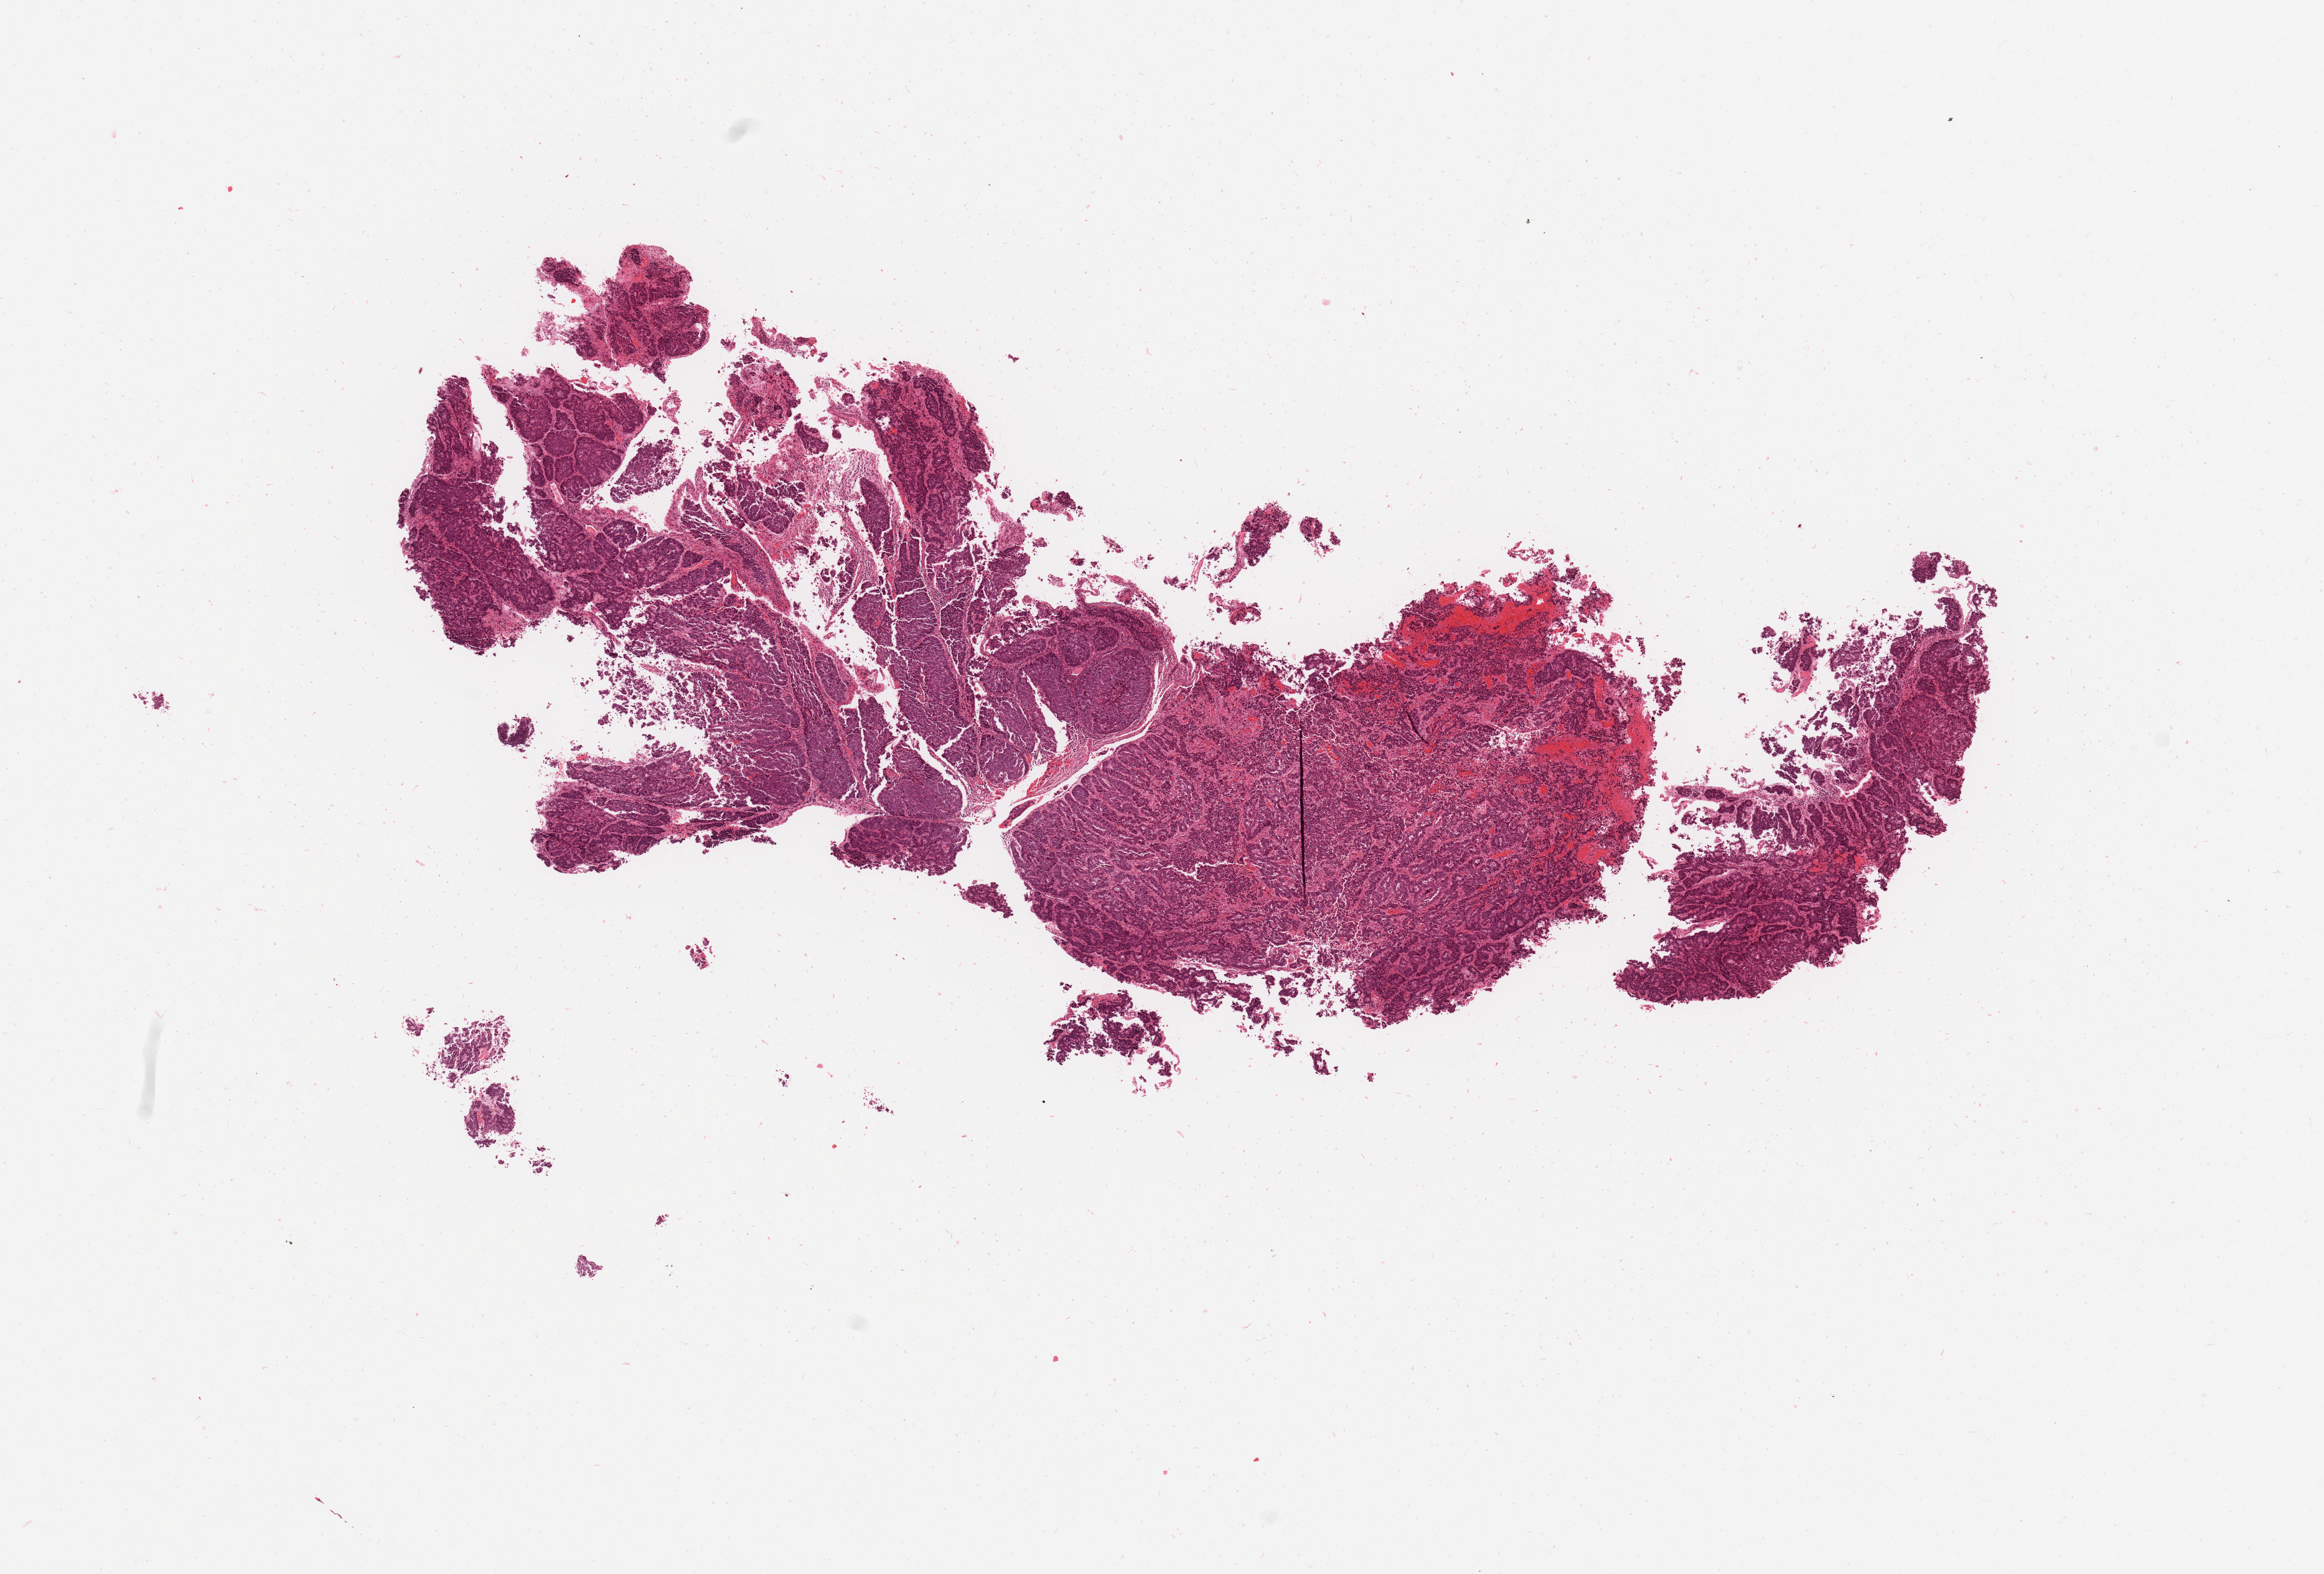
Whole-slide histology image, H&E-stained — whole scanned area (about 14.8 x 10.0 mm) shown as a low-resolution overview, tumour tissue sample, sampled site: uterus. Patient: female, age 73 years. Pathologist review of this section (percent, as recorded): tumour nuclei 90%, necrosis 2%.
Histologic diagnosis: Endometrioid adenocarcinoma, NOS.